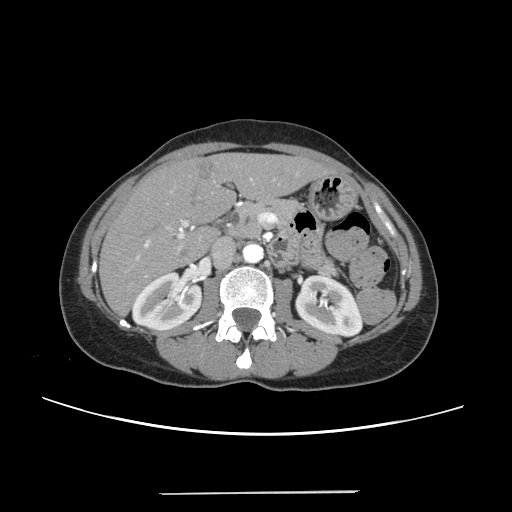
Contrast-enhanced abdominal CT, one axial slice; slice 118 of 240 in the series (ordered by position); 120 kVp; intravenous contrast given; soft-tissue window (W 400 / L 40 HU); 1.25 mm slice thickness; 512 × 512 image matrix. Female patient, age 60 years. From the clinical record (not read from this slice): diagnosis: colorectal cancer liver metastases, imaged before liver resection; multiple liver metastases: no.
Structures marked on this image (expert manual segmentation):
- liver: box from (x=101, y=153) to (x=329, y=313) px
- planned liver remnant (the part of the liver to remain after resection): (x=101, y=154)–(x=329, y=313)
- portal vein (with intrahepatic branches): (x=136, y=178)–(x=254, y=259)
- liver metastasis: (x=197, y=161)–(x=215, y=181)